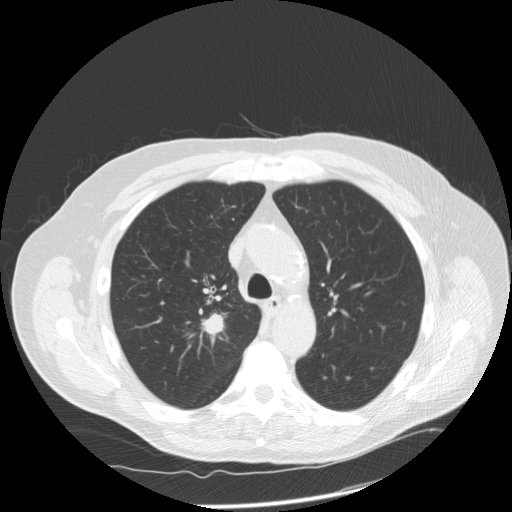
Axial slice from a low-dose chest CT screening exam, third annual screen, lung window (W 1500 / L -600 HU), standard (soft-tissue) reconstruction kernel (STANDARD), 512 × 512 image matrix, field of view 390 × 390 mm. Male, age 69 years at enrolment. Former smoker at enrolment.
• Expert reader's lesion annotation, box from (x=183, y=302) to (x=242, y=351) px.
• Reader record for this screening exam (exam-level; its link to the box is not recorded): non-calcified nodule or mass ≥4 mm, right upper lobe, 18 × 17 mm, spiculated (stellate) margins, soft tissue attenuation, pre-existing on the prior screen: no.
• Lung cancer was diagnosed 13 days after this screen: squamous cell carcinoma, NOS, right upper lobe, poorly differentiated (G3), stage IA (AJCC 6th edition), 22 mm at pathology.